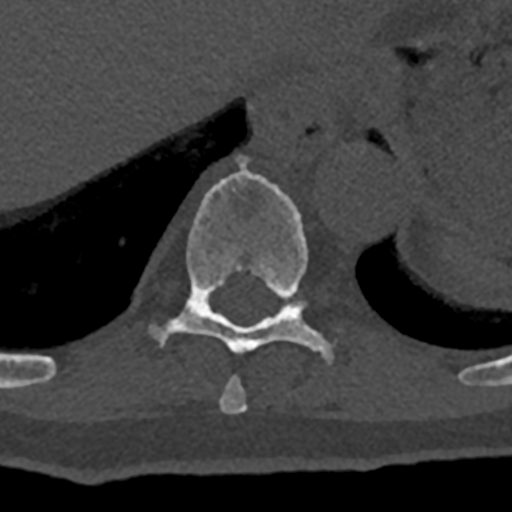
CT including the spine, one axial slice. Position 601 of 797 along the scan axis. Reconstruction kernel Br40s/3. Bone window (W 1800 / L 400 HU). 0.5 mm slice thickness. 512 × 512 image matrix, field of view 160 × 160 mm. Male patient, age 74 years. From the clinical record (not read from this slice): primary cancer: renal; vertebrae with lytic lesions (as recorded): T10, L1, L2, L3, L4, L5.
Structures marked on this image (semi-automatic segmentation, software-assisted and operator-edited):
- T10 vertebra: bounding box [x1, y1, x2, y2] px = [151, 156, 331, 361]
- T11 vertebra: [284, 298, 306, 309]
- T9 vertebra: [219, 376, 248, 413]